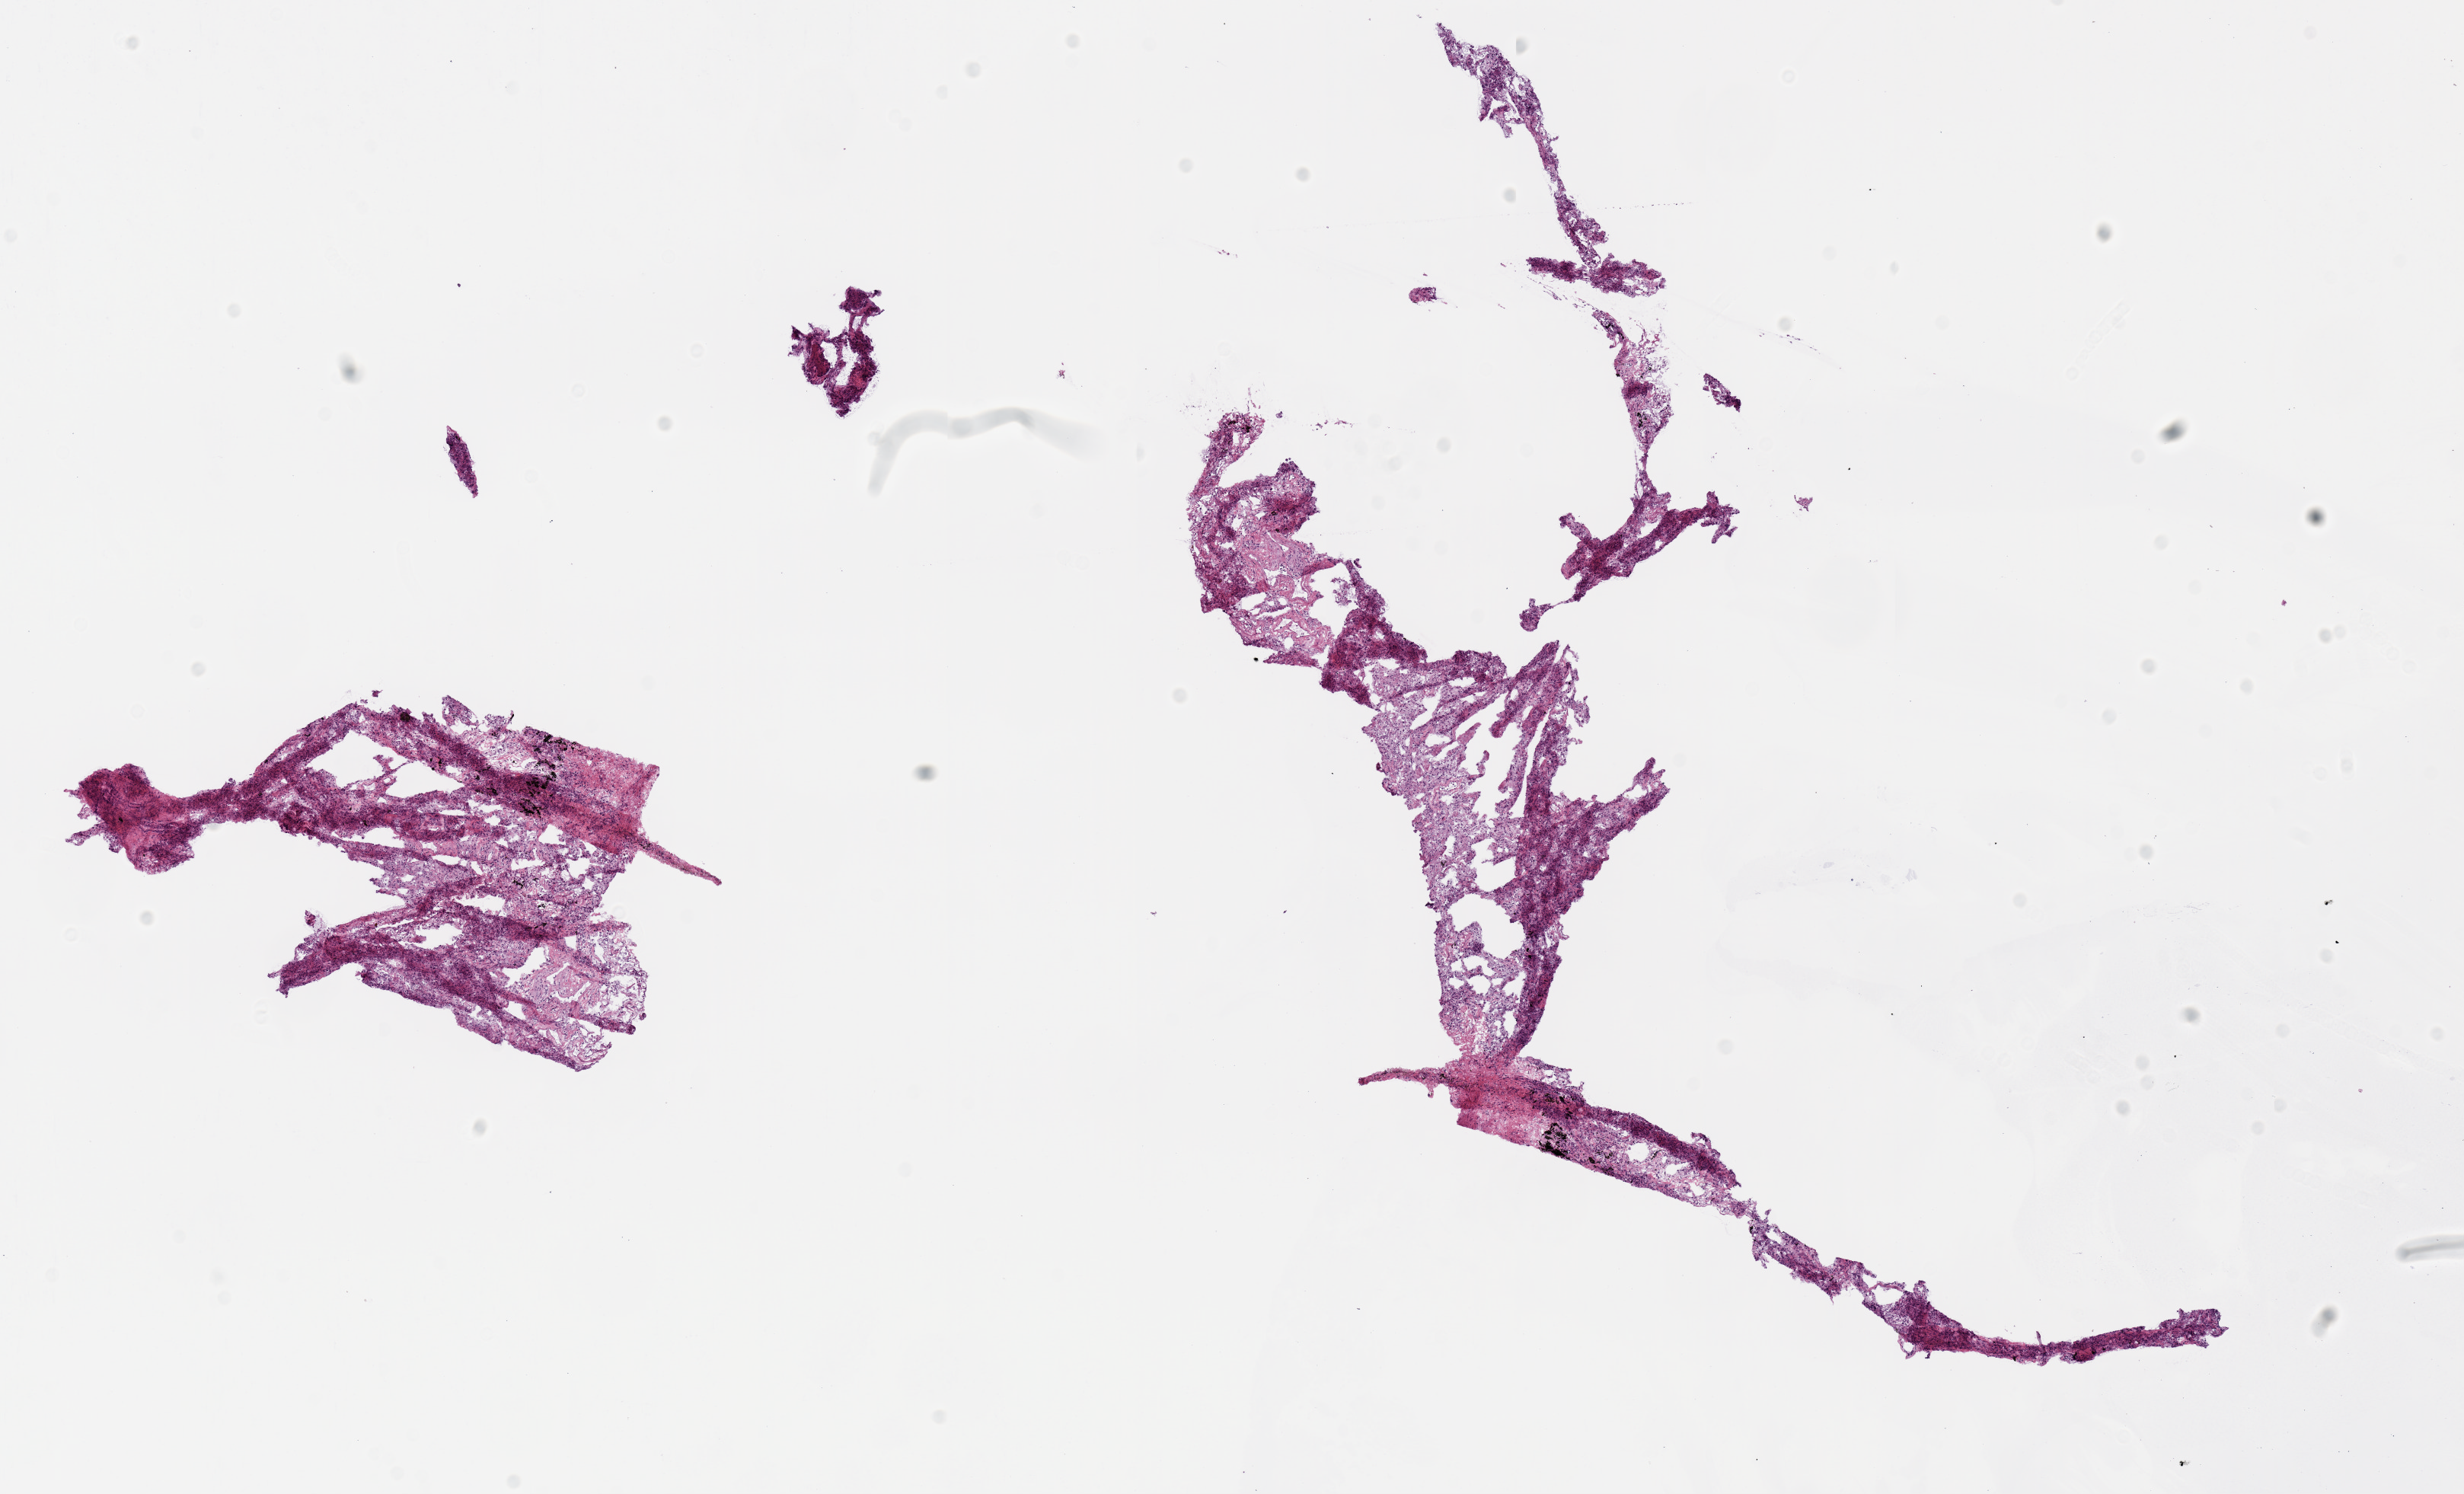
Hematoxylin and eosin (H&E) stained whole-slide image, low-resolution overview of the scanned area, about 12.8 x 7.8 mm (from a 20x scan), frozen section from the top of the tissue portion, lung, solid tissue normal (non-tumour tissue) sample. Male patient; age at initial diagnosis 72 years.
This section: solid tissue normal (non-tumour) sample from the same patient. Patient diagnosis: Papillary adenocarcinoma, NOS (upper lobe, lung).